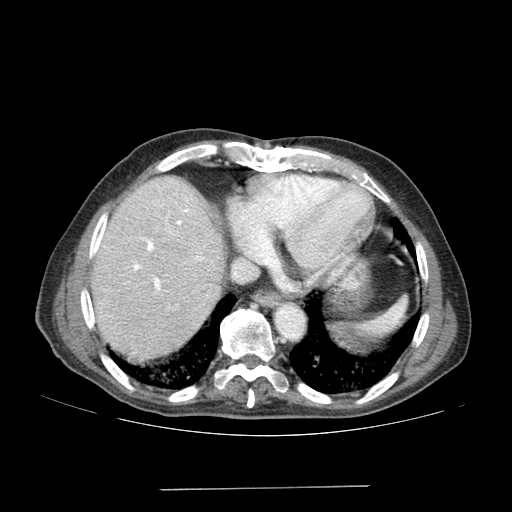
Contrast-enhanced abdominal CT (liver protocol), one axial slice; slice 146 of 192 in the series (ordered by position); reconstruction kernel SOFT; 120 kVp; soft-tissue window (W 400 / L 40 HU); 2.5 mm slice thickness; 512 × 512 image matrix, field of view 400 × 400 mm. Case-level facts recorded for this patient, not image findings: diagnosis: hepatocellular carcinoma (patient treated with transarterial chemoembolisation; whether this scan precedes or follows treatment is not stated here); TNM stage (as recorded): Stage-IVA; Child-Pugh class: A.
Annotated regions visible in this slice (semi-automatic segmentation, software-assisted and operator-edited):
- liver parenchyma outside the tumour (the mass and vessels are separate outlines, so this box may not span the whole liver): bounding box (x1, y1, x2, y2) in pixels: (90, 176, 224, 360)
- liver vessels: (134, 209, 202, 290)